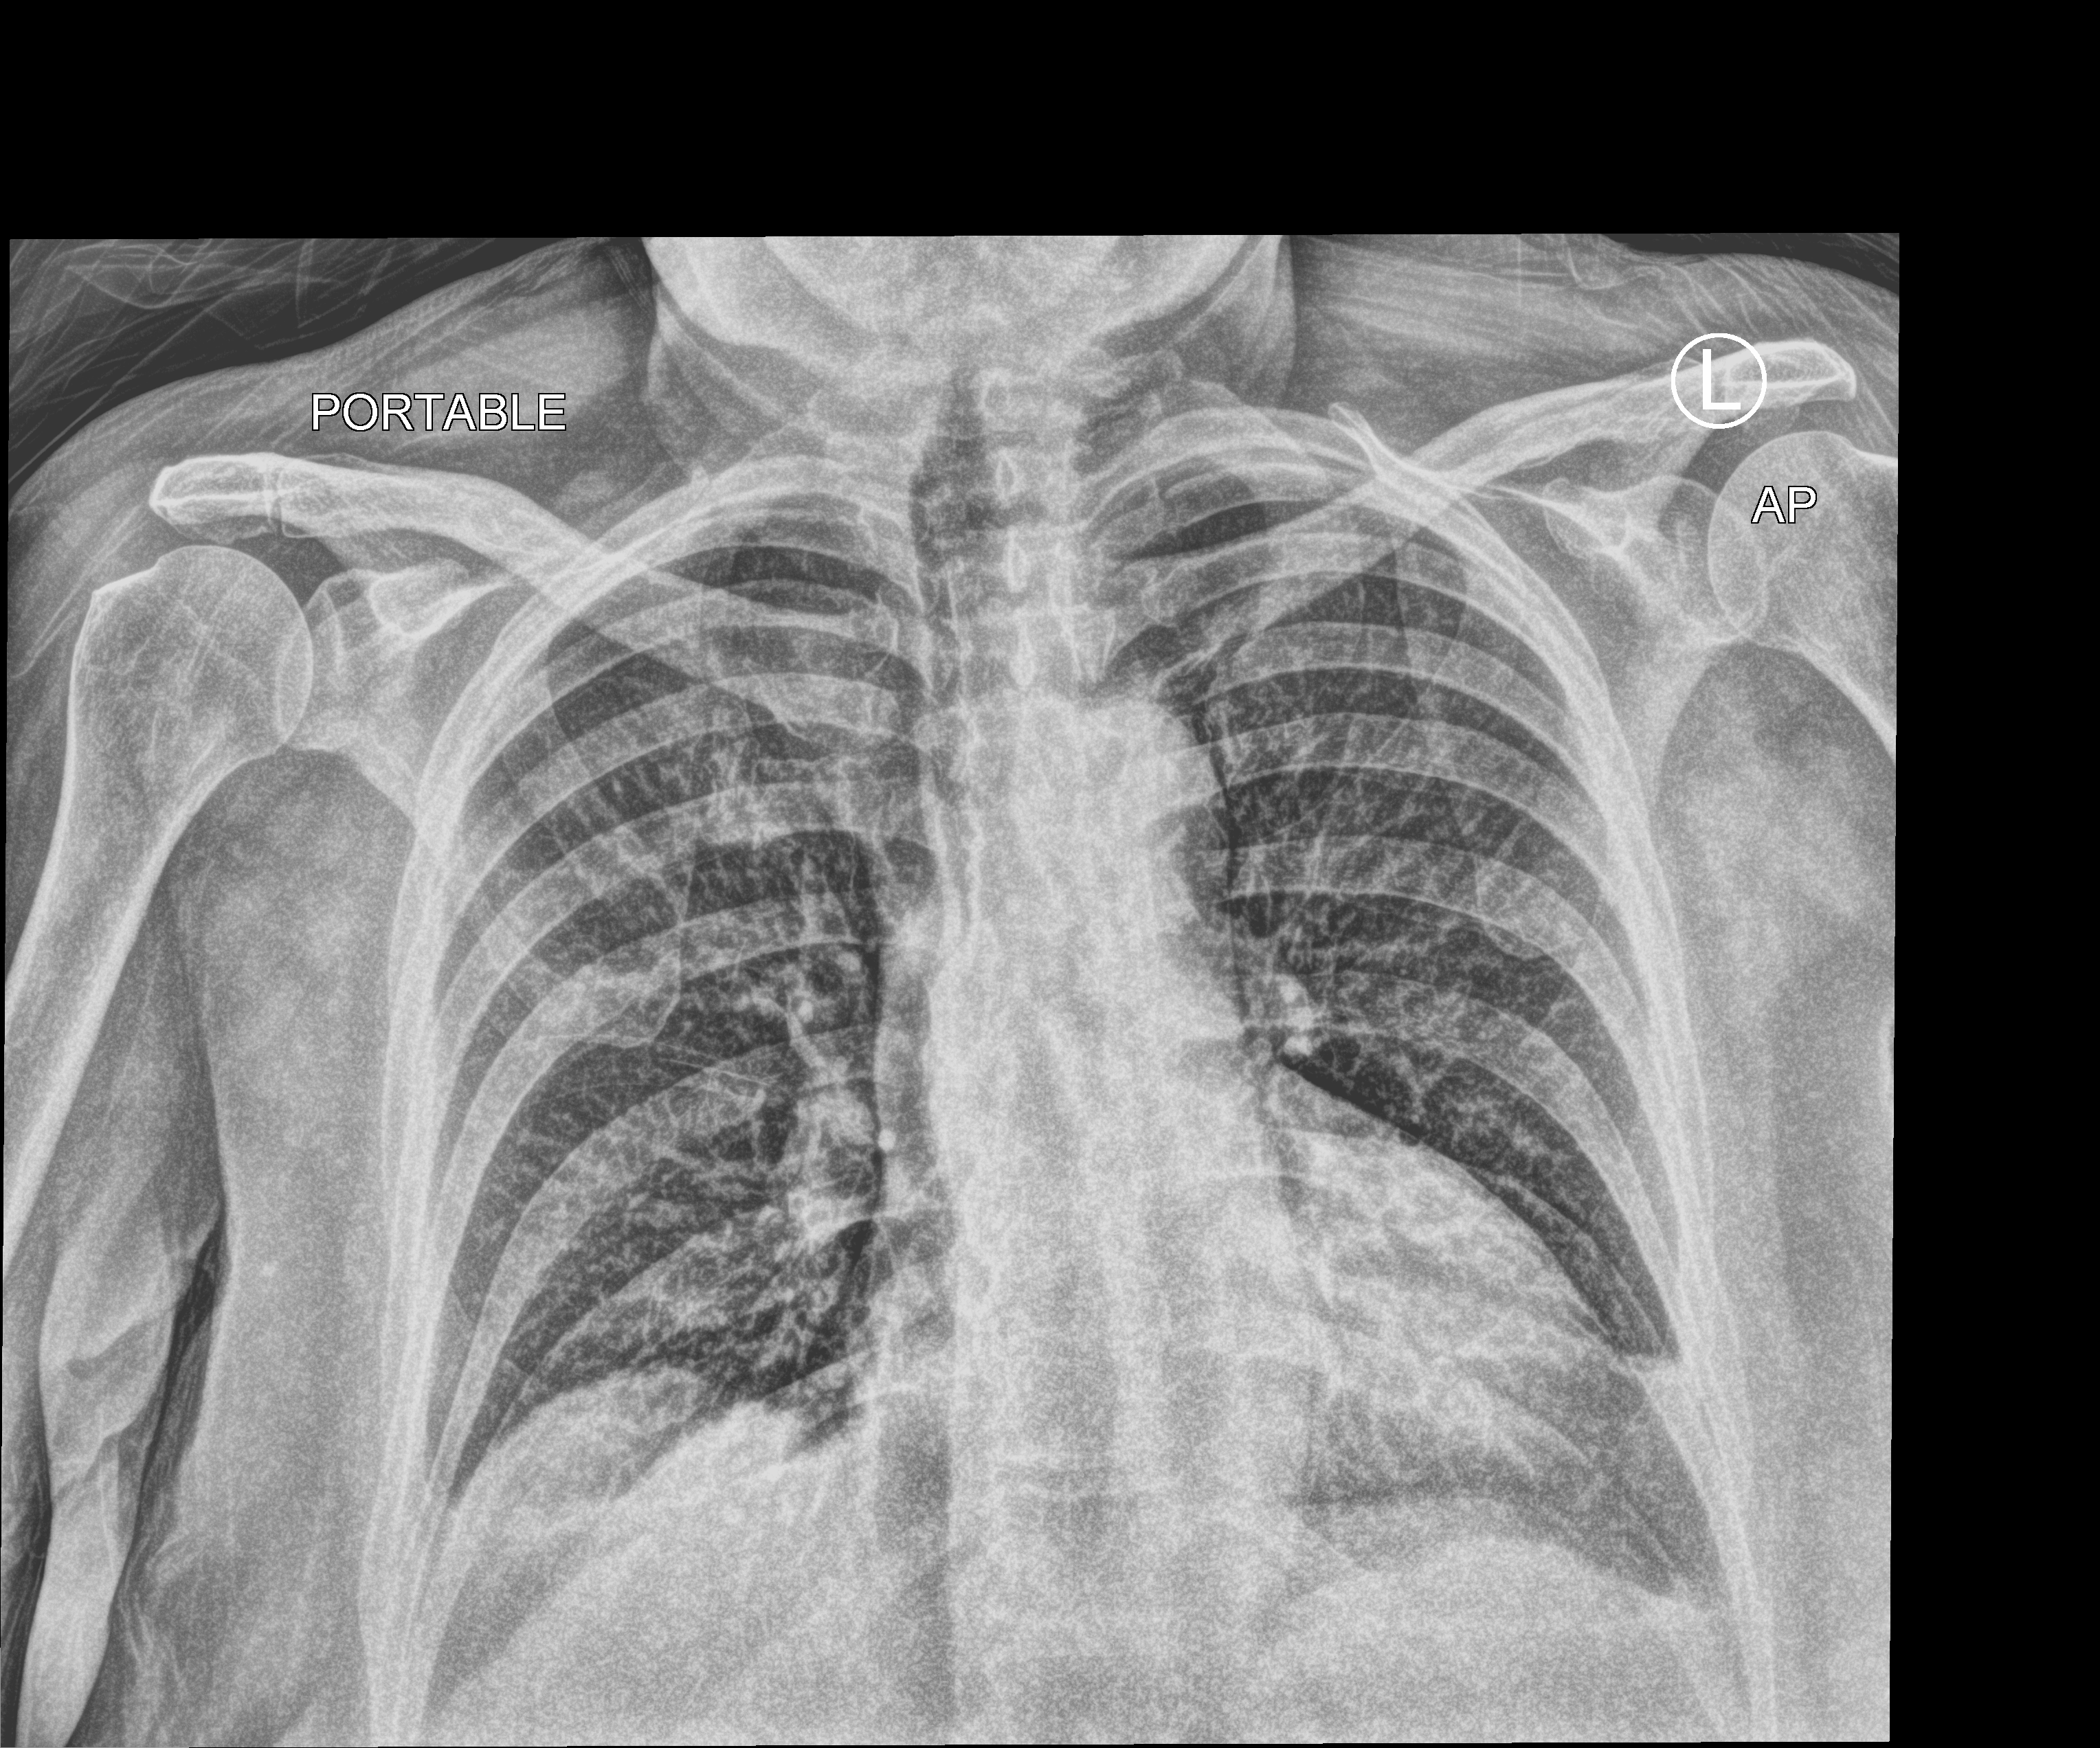
Bedside chest radiograph (computed radiography); anteroposterior (AP) projection. Patient hospitalised with COVID-19; female, aged 75–90 years.
From the hospital-stay record, not from the radiograph (when in the stay this image was taken is not recorded): length of hospital stay: 1 day.